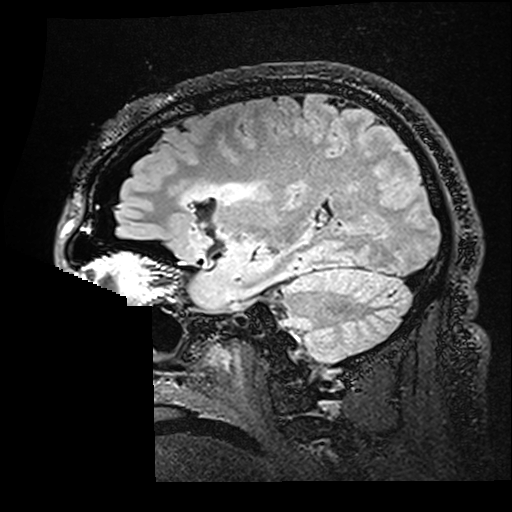
Brain MRI from a brain-tumour surgery series, one sagittal slice. Slice 116 of 176 in the series (ordered by position). T2 FLAIR. 1 mm slice thickness. 512 × 512 image matrix, field of view 250 × 250 mm. From the clinical record (not read from this slice): histopathology: Astrocytoma; WHO grade: 2; IDH mutation: yes.
Structures marked on this image (outlined manually by an expert reader):
- residual tumour: bounding box (x1, y1, x2, y2) in pixels: (181, 182, 248, 207)